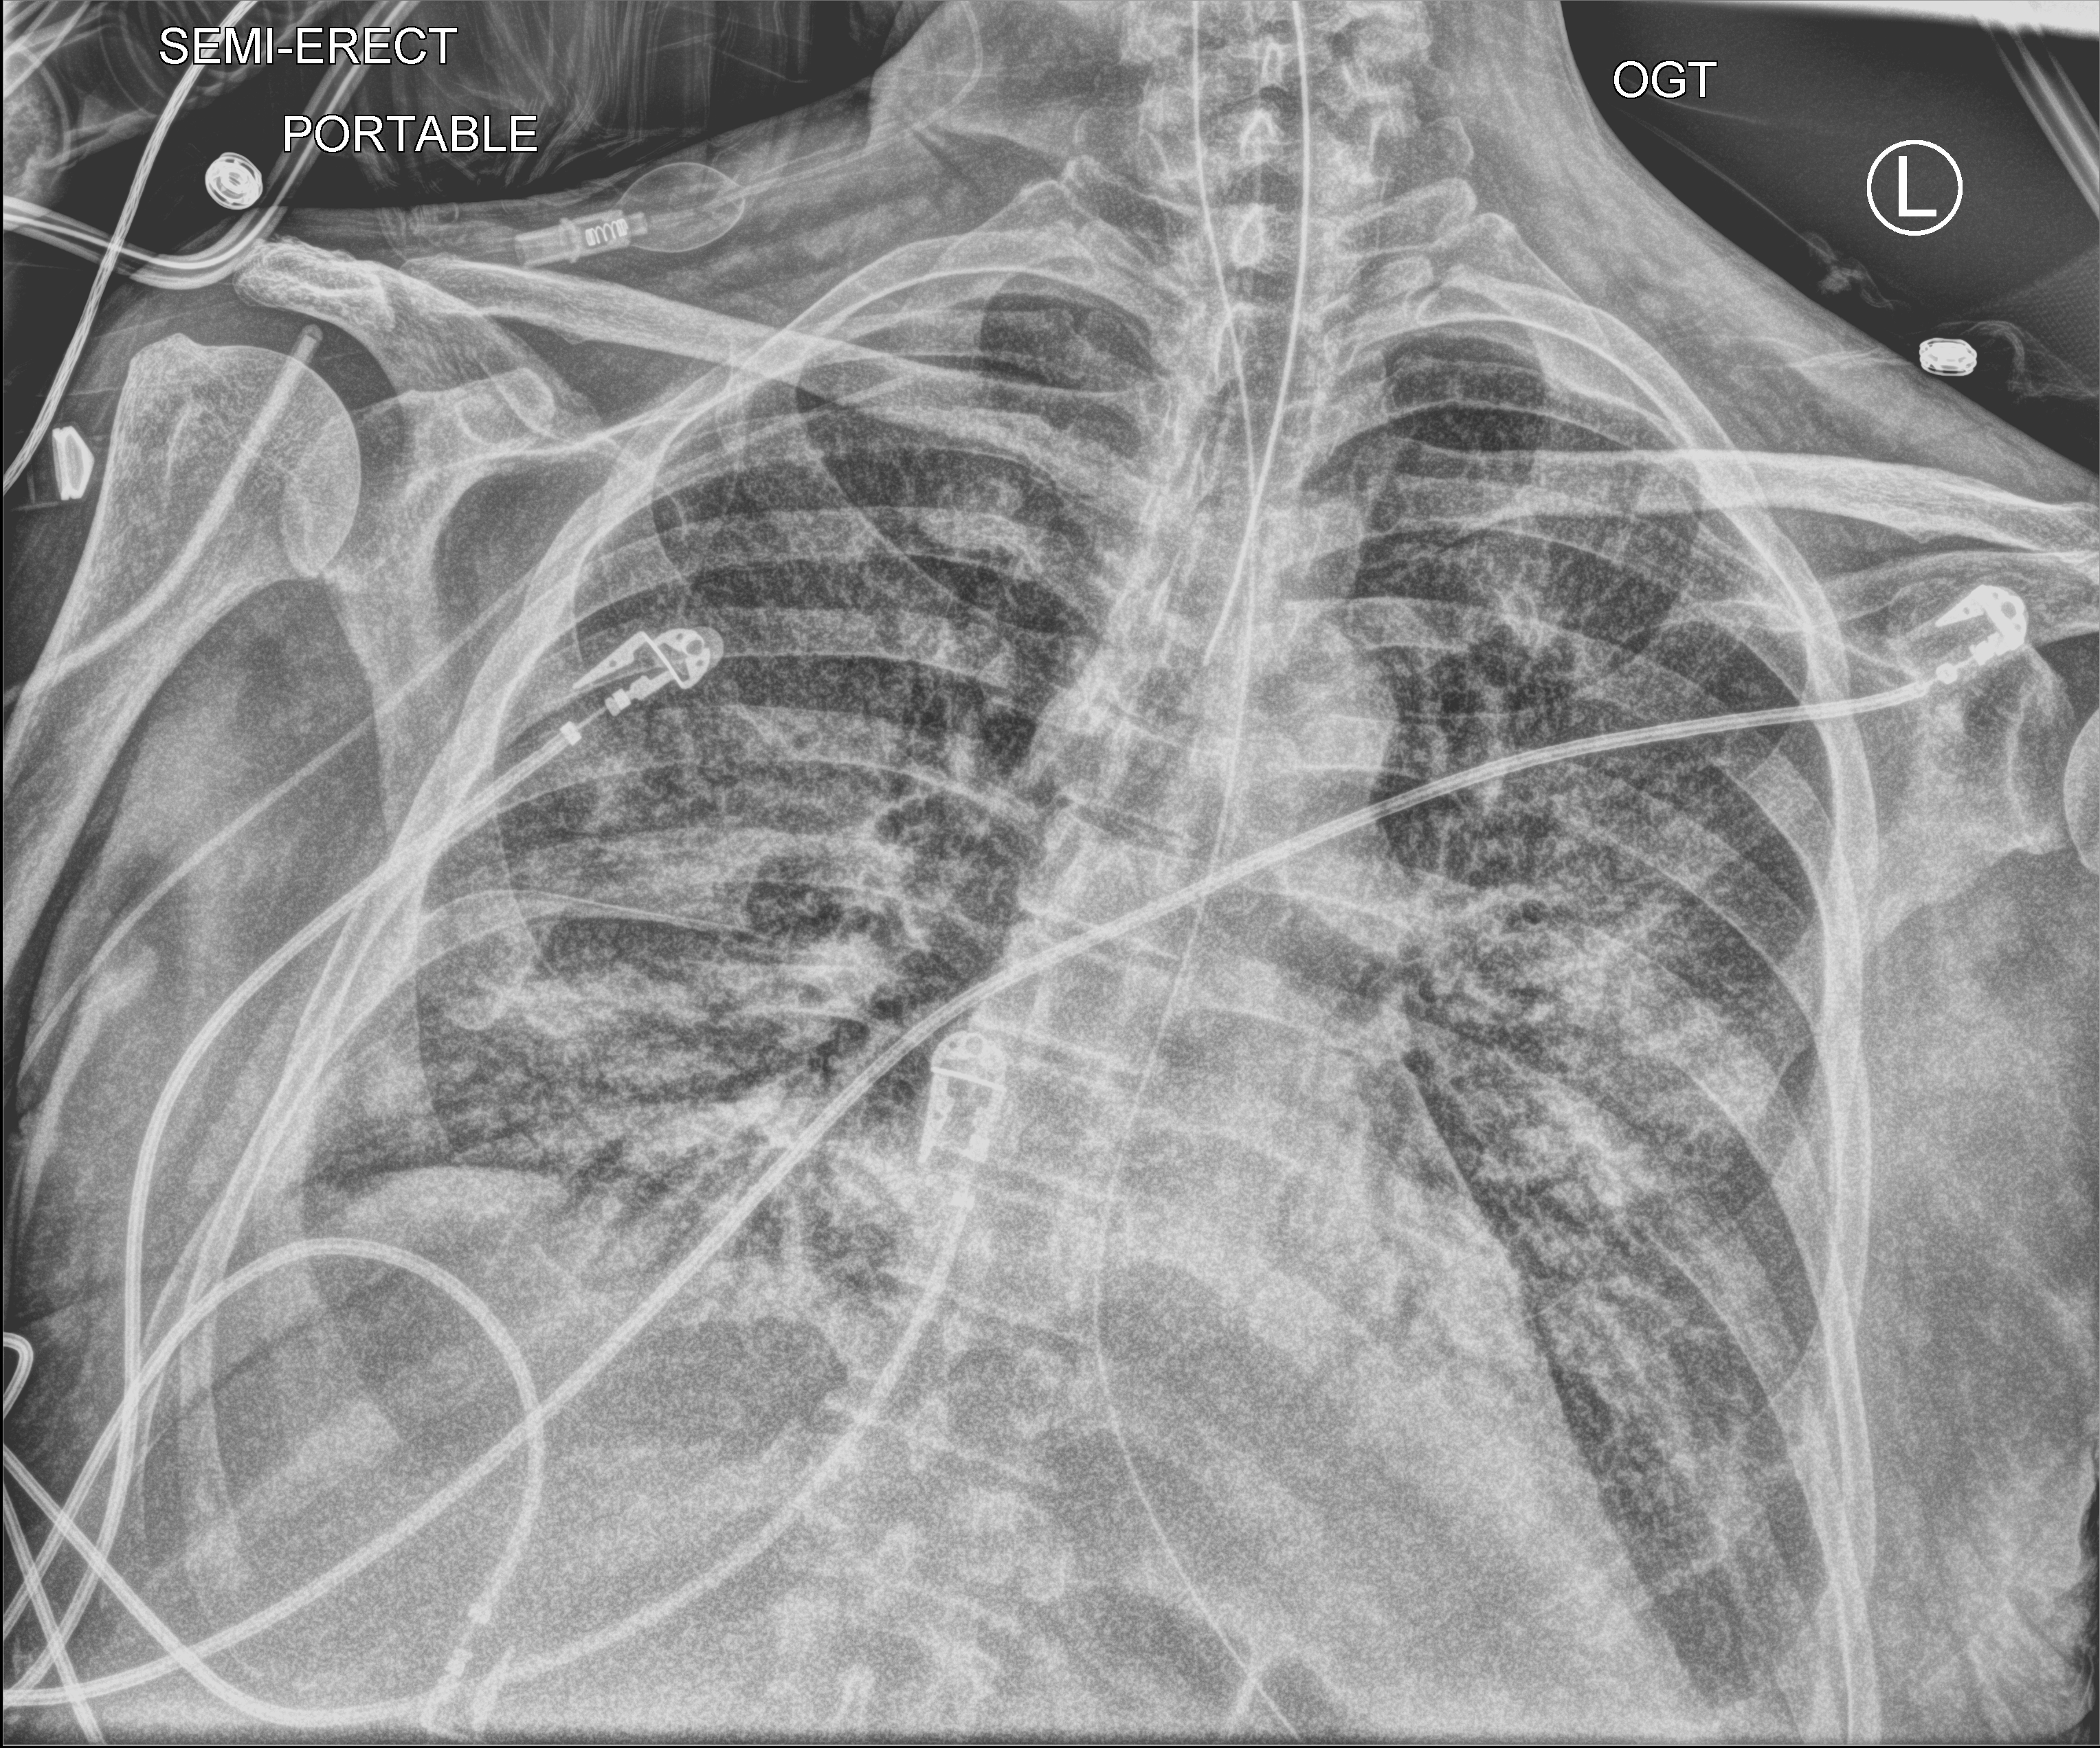
Portable chest radiograph, anteroposterior (AP) projection. Male patient hospitalised with COVID-19, age 60–74 years.
Admission-level facts for this patient (not findings on this image; timing relative to this image not recorded):
- admitted to intensive care during this hospital stay: yes